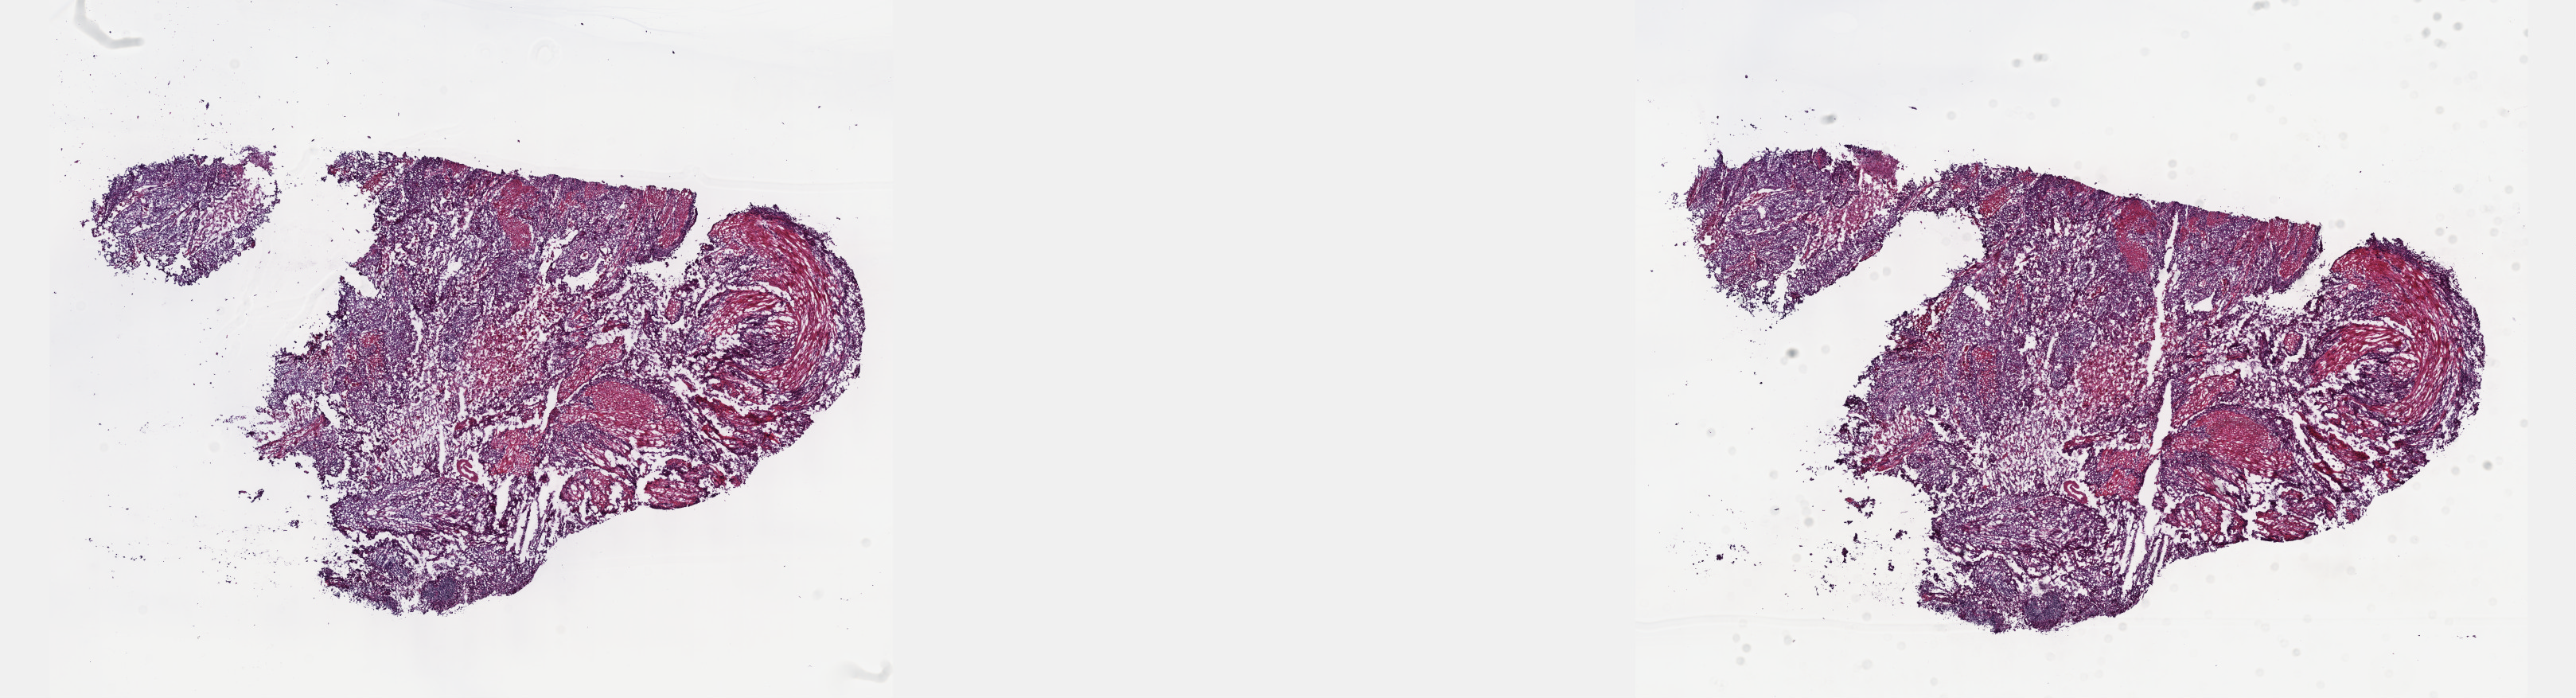
Whole-slide histology image, H&E — shown as a low-resolution overview of the whole scanned area (about 26.2 x 7.1 mm), frozen section from the top of the tissue portion, sample: primary tumour, bladder. Male patient; age at initial diagnosis 73 years. Histologic grade: high grade. Pathologist review of this section (percent, as recorded): tumour cells 70%, tumour nuclei 85%, normal cells 0%, stromal cells 15%, necrosis 15%. Inflammatory infiltration, as recorded: lymphocyte infiltration 0%, monocyte infiltration 0%, neutrophil infiltration 0%.
AJCC pathologic stage: II (7th edition). Histologic diagnosis: Transitional cell carcinoma. TNM: T2 NX M0.